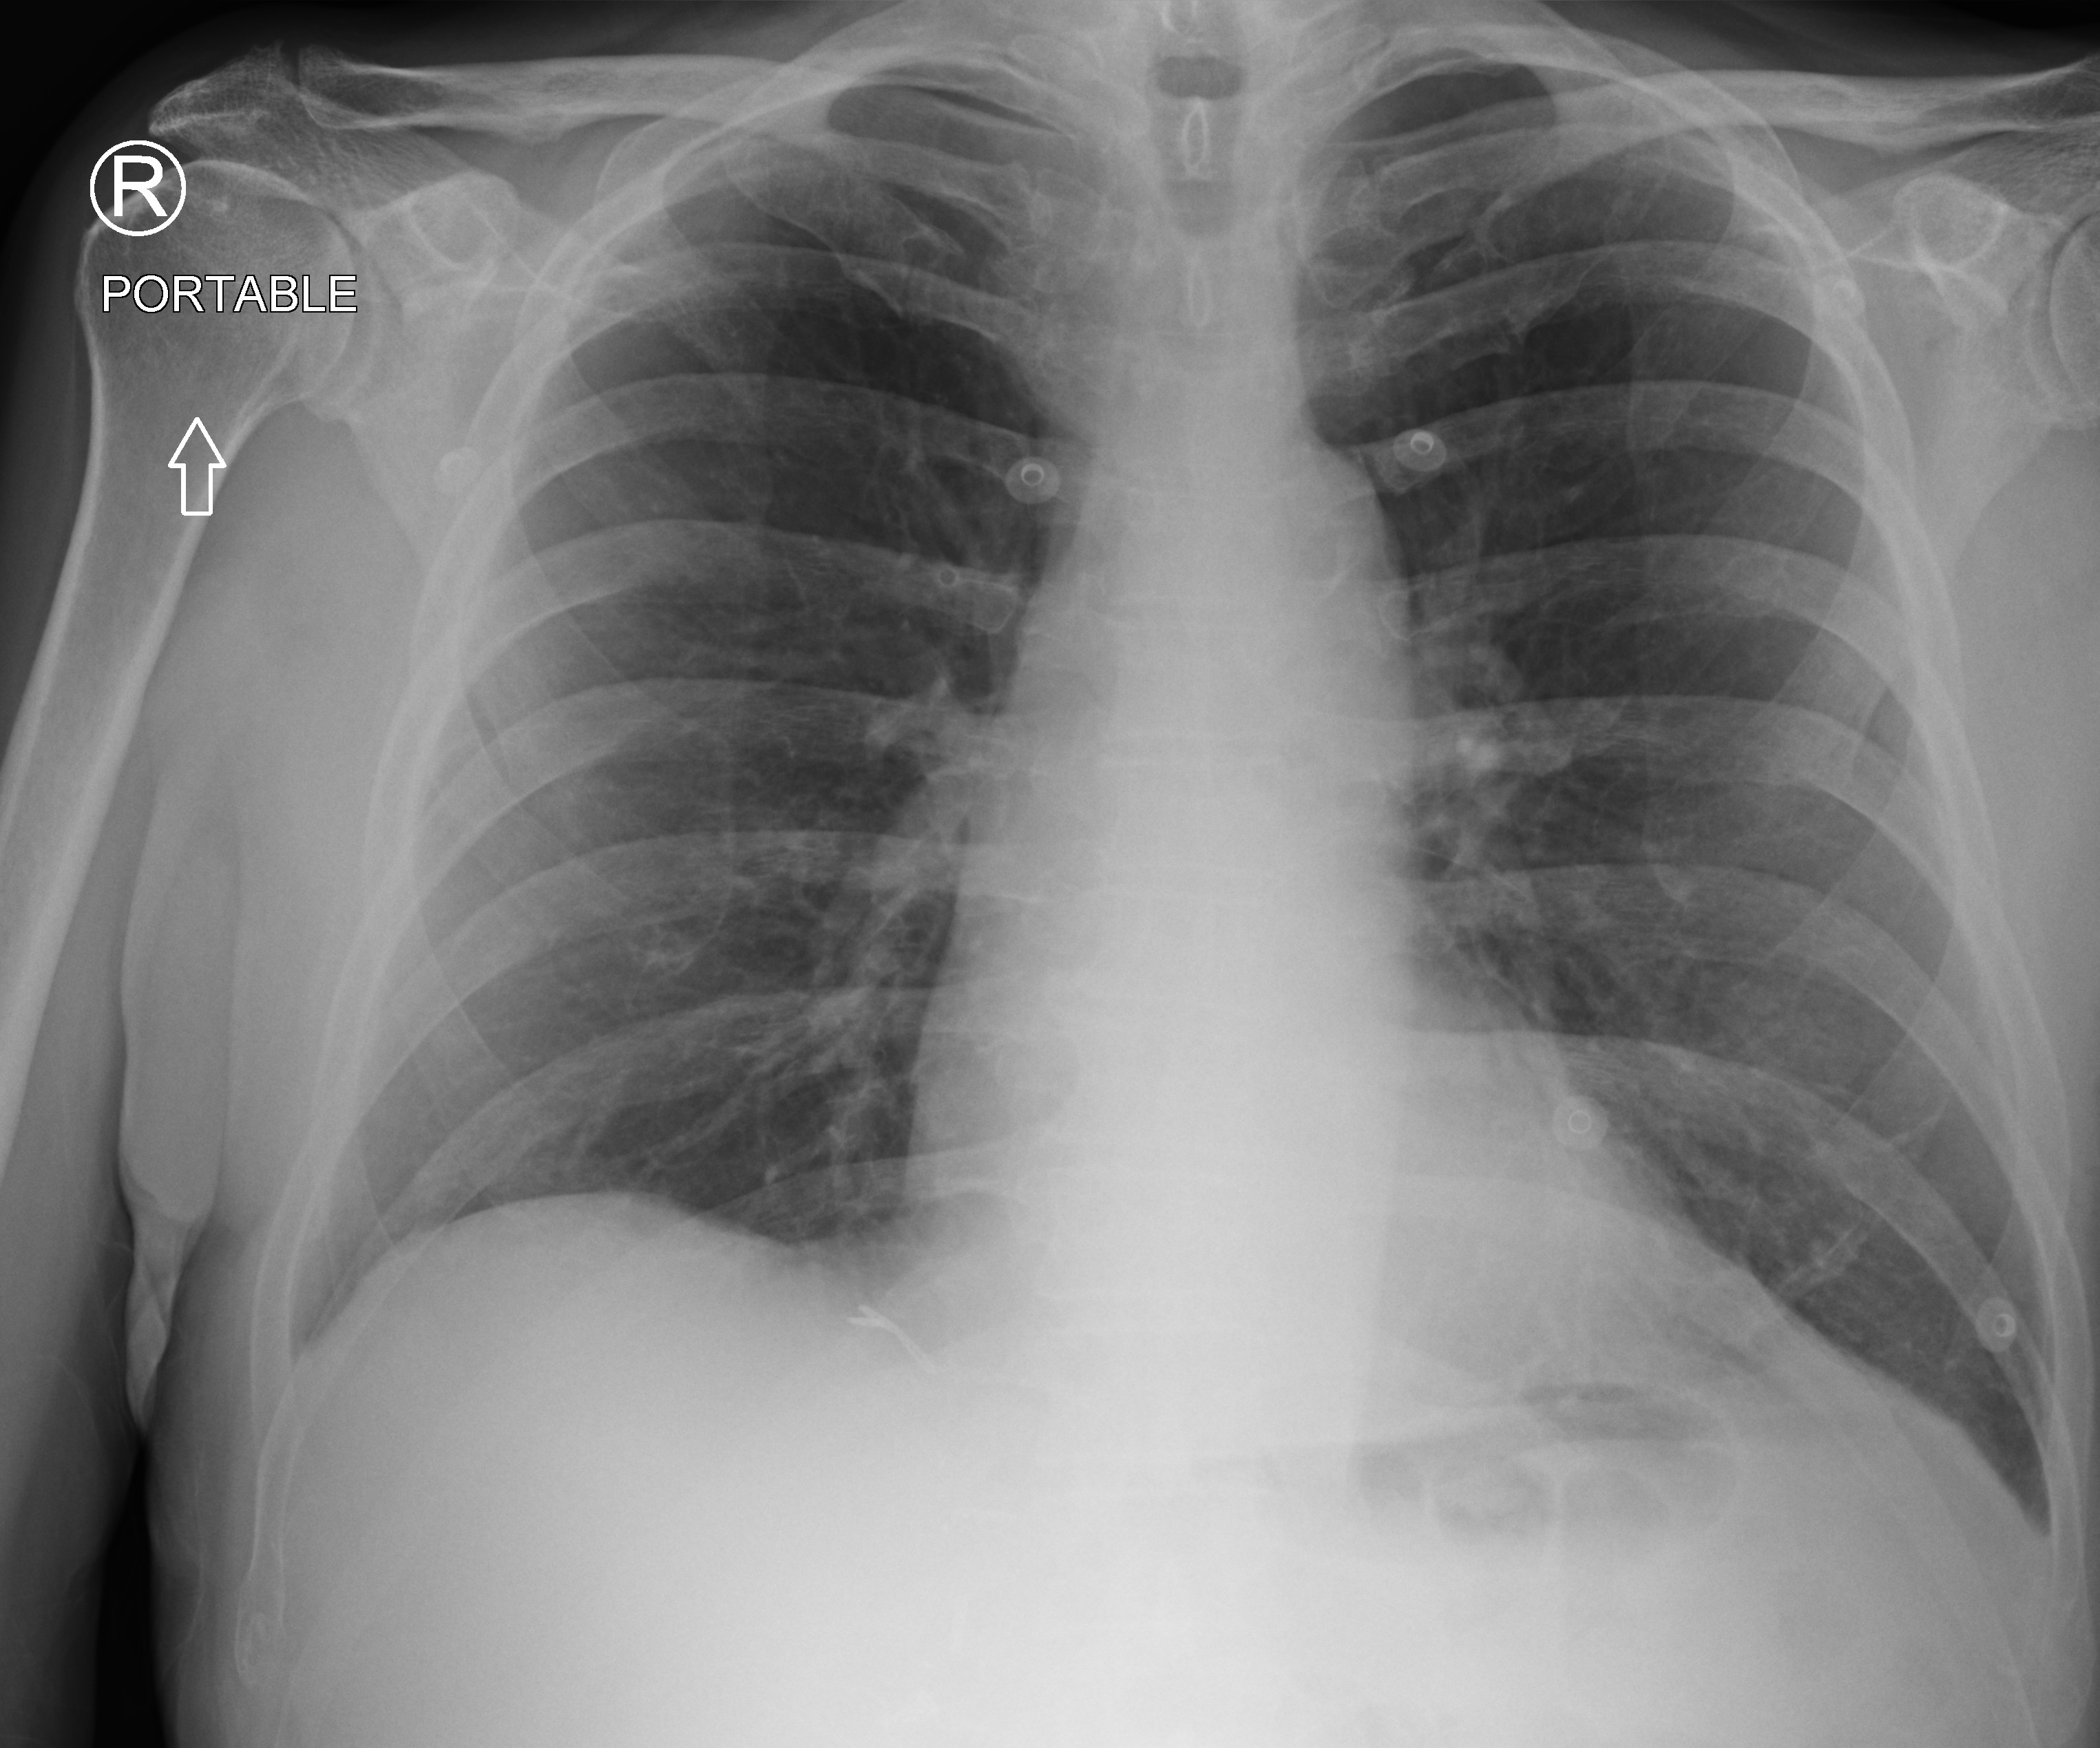
Chest X-ray (portable). Patient hospitalised with COVID-19; male, aged 60–74 years.
Admission-level facts for this patient (not findings on this image; timing relative to this image not recorded): mechanically ventilated during this hospital stay: no; admitted to intensive care during this hospital stay: no.